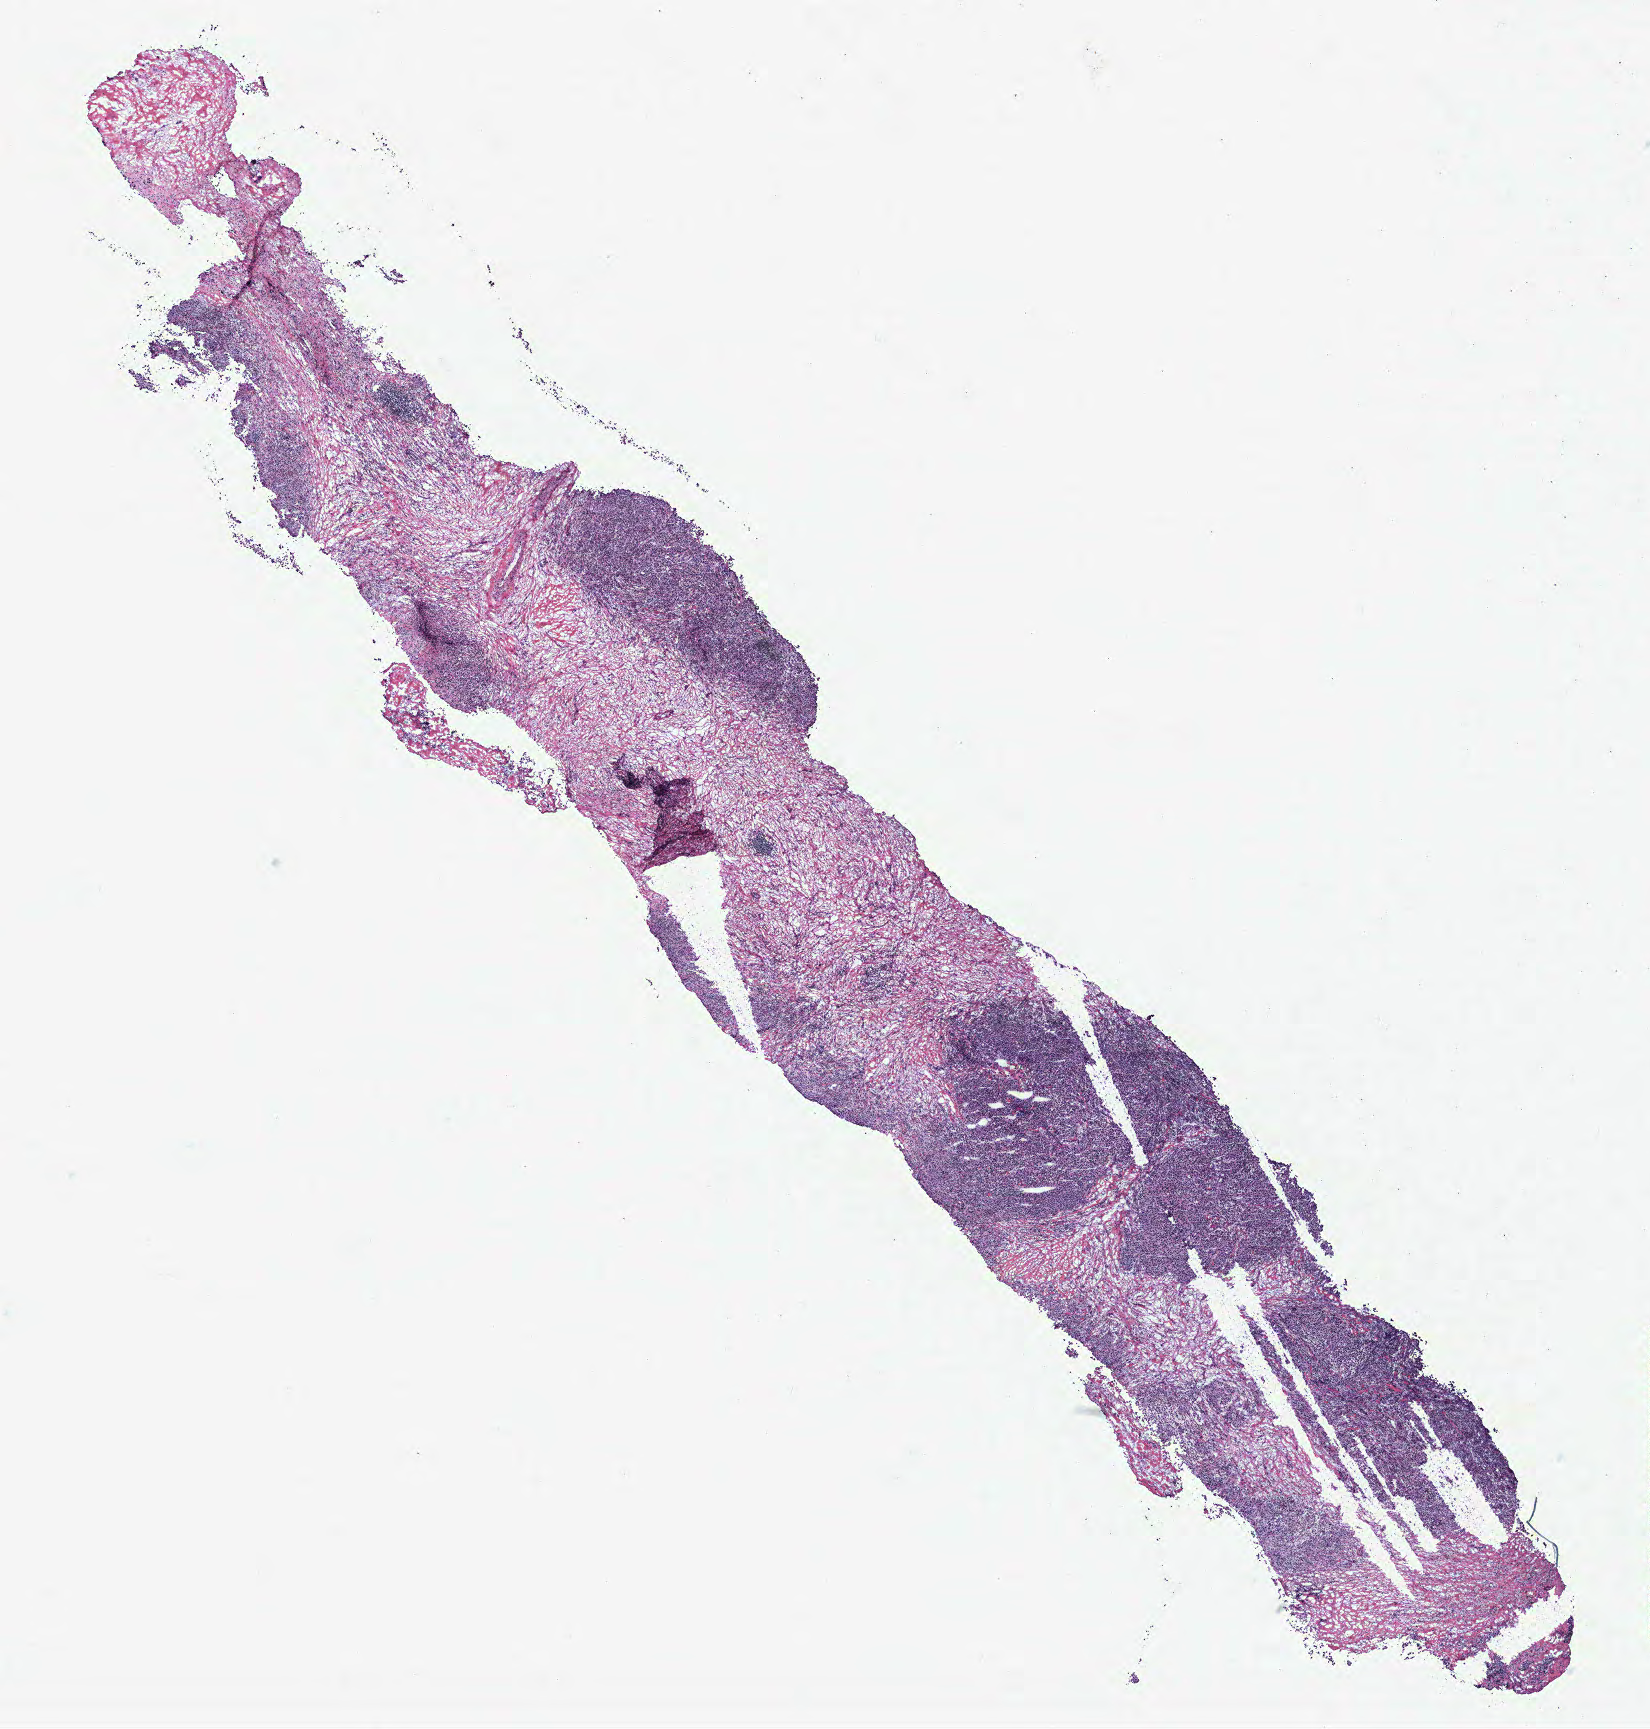
Digitized H&E-stained tissue section (whole slide) — shown as a low-resolution overview of the whole scanned area (about 13.2 x 13.8 mm); breast, tissue type not recorded. 83-year-old female patient.
* patient diagnosis: Infiltrating duct carcinoma, NOS